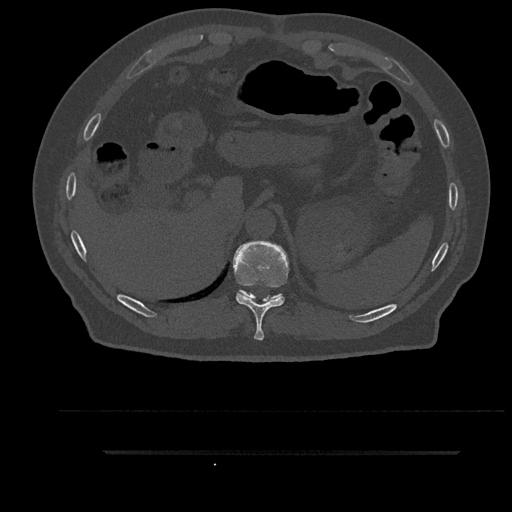
CT including the spine, one axial slice; slice 347 of 797 in the series (ordered by position); 120 kVp; bone window (W 1800 / L 400 HU); 0.5 mm slice thickness; 512 × 512 image matrix, field of view 432 × 432 mm. Male patient, age 63 years. From the clinical record (not read from this slice): primary cancer: renal; vertebrae with lytic lesions (as recorded): T8.
Outlined on this slice (semi-automatically segmented with operator editing):
- T10 vertebra: bounding box [x1, y1, x2, y2] px = [232, 241, 289, 341]
- T11 vertebra: [238, 290, 282, 300]